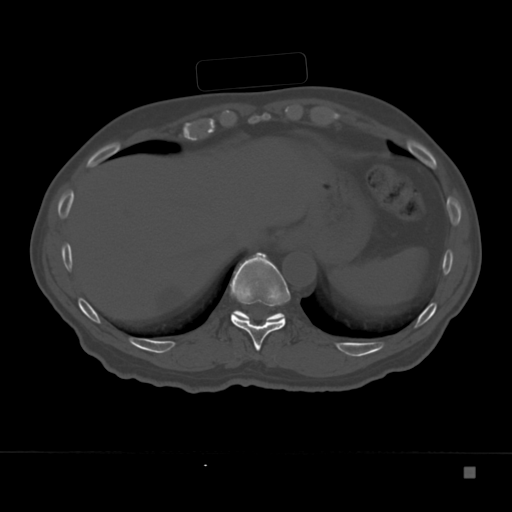
CT including the spine, one axial slice. Position 167 of 332 along the scan axis. Reconstruction kernel Br40s. 120 kVp. Bone window (W 1800 / L 400 HU). 1.5 mm slice thickness. 512 × 512 image matrix, field of view 389 × 389 mm. Male patient, age 72 years. From the clinical record (not read from this slice): primary cancer: skeletal.
Structures marked on this image (semi-automatically segmented with operator editing):
- T10 vertebra: bounding box (x1, y1, x2, y2) in pixels: (230, 252, 290, 351)
- T11 vertebra: (233, 310, 285, 321)